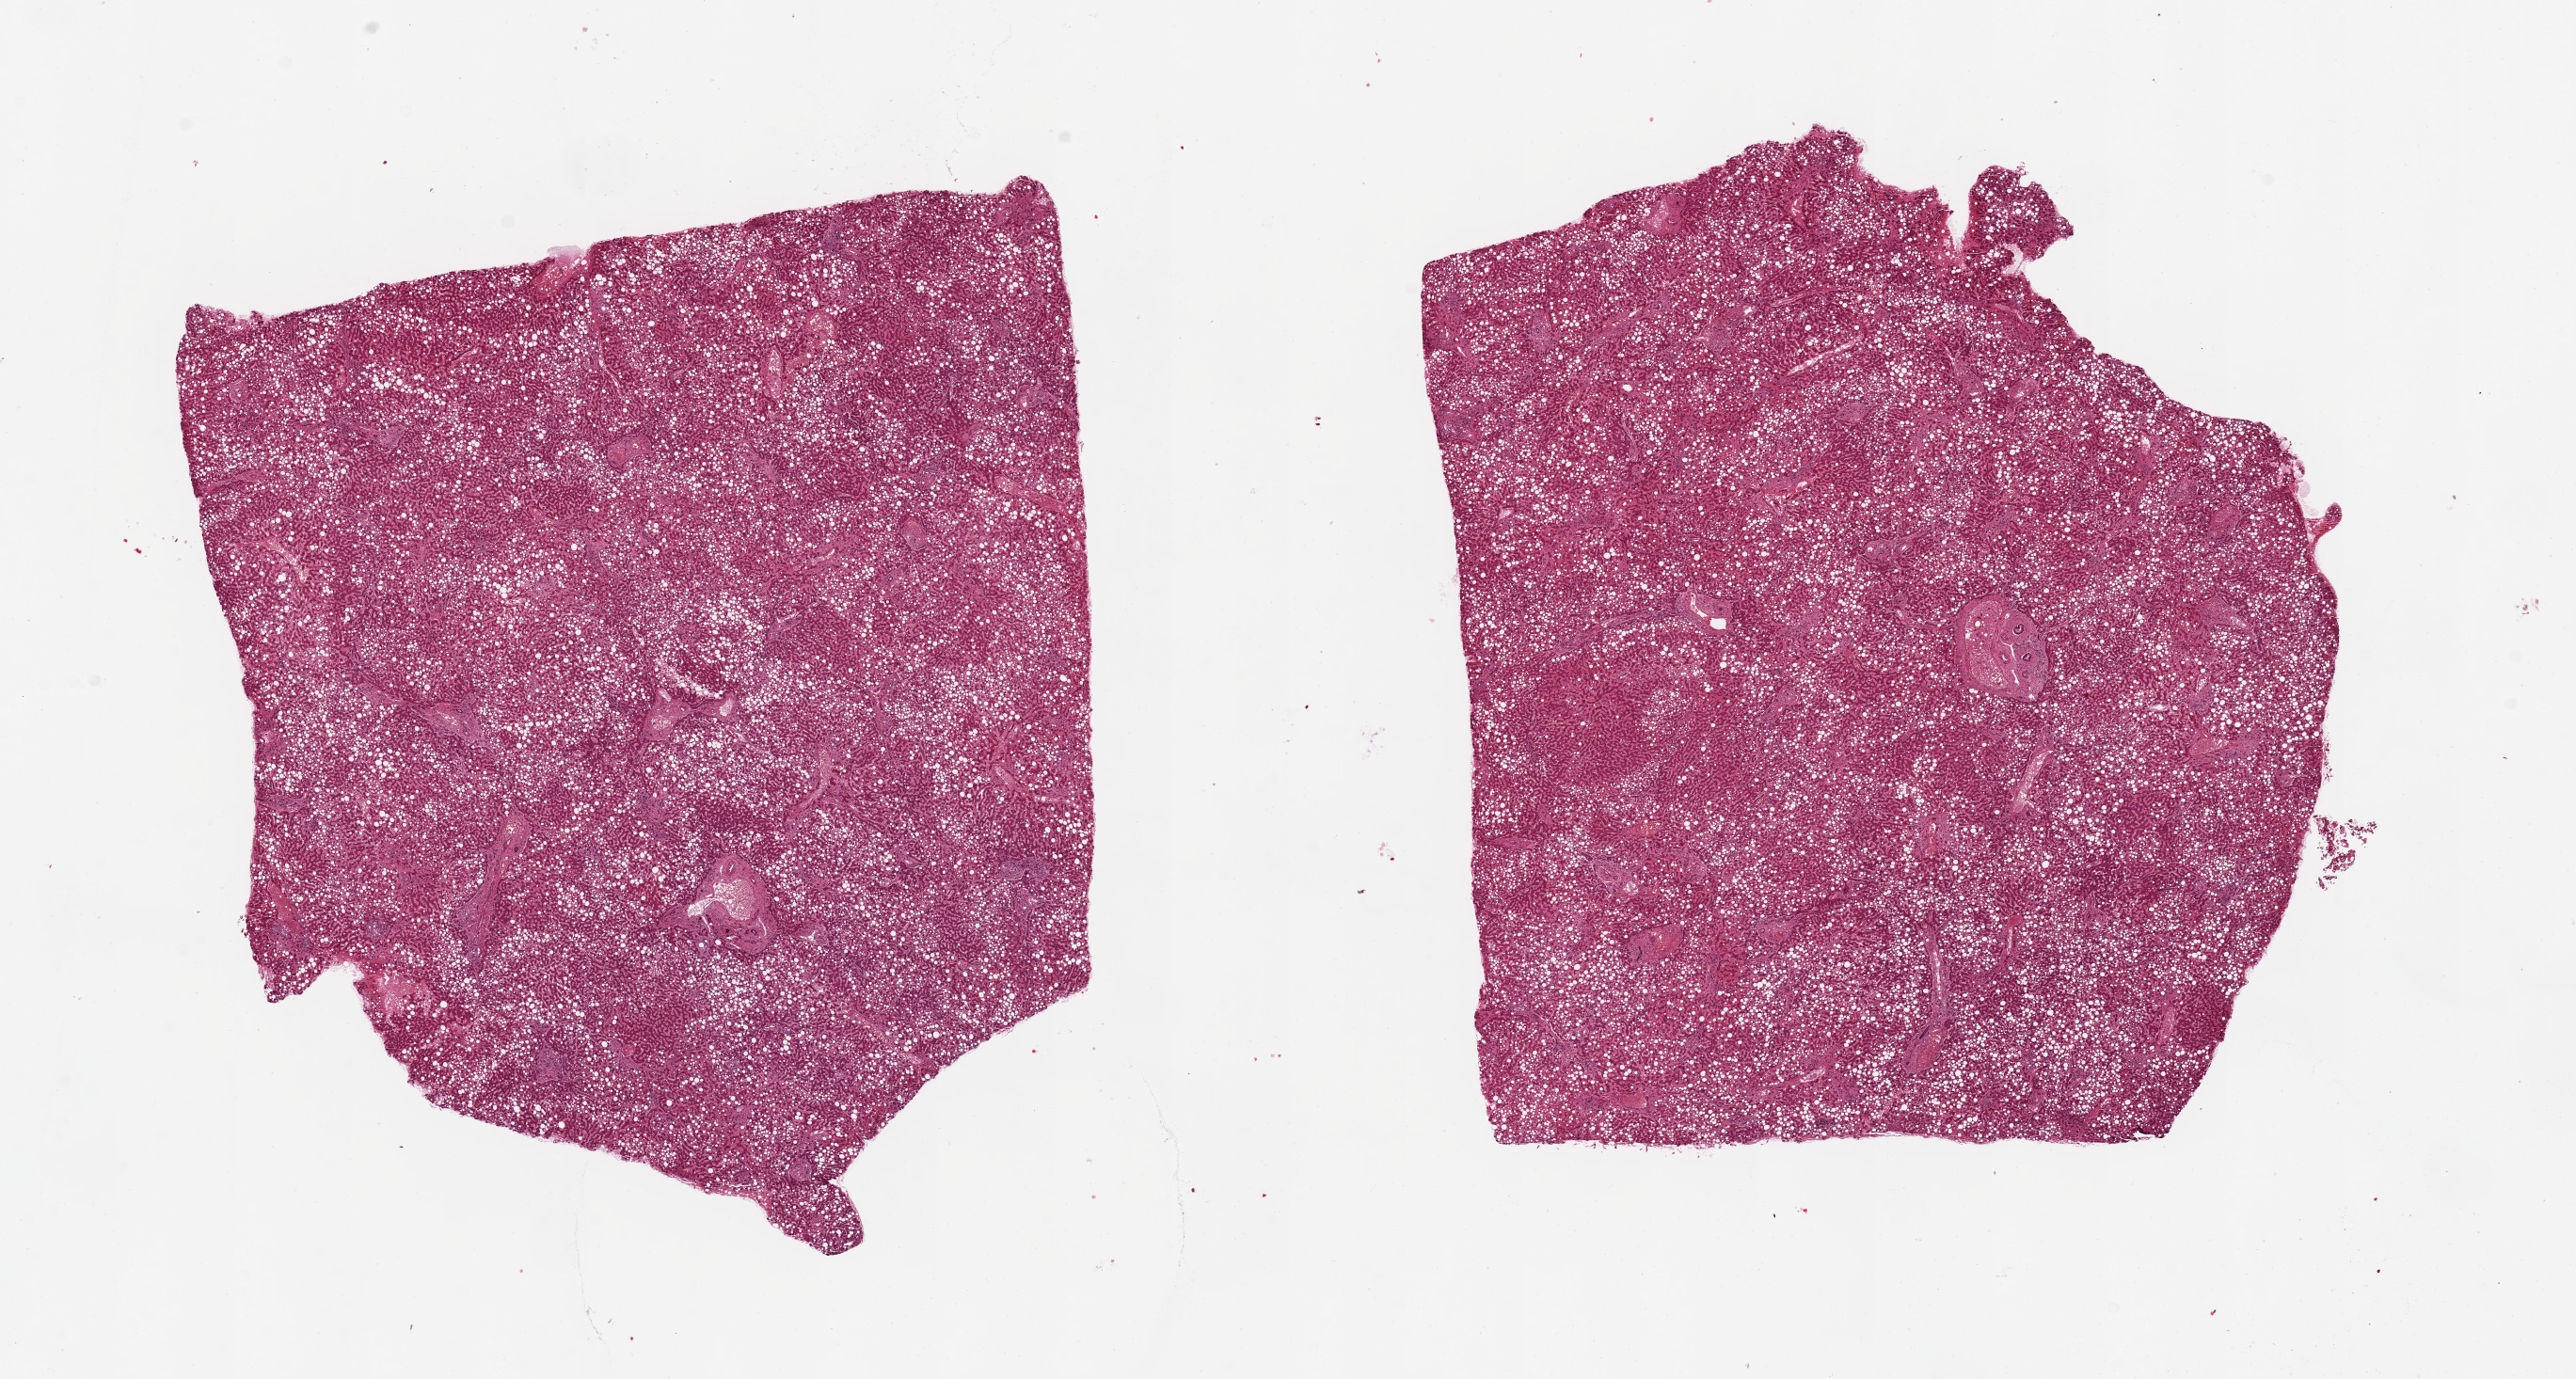
Digitized hematoxylin and eosin (H&E)-stained section, brightfield — low-resolution overview of the scanned area, about 21.7 x 11.6 mm (slide scanned at 20x). PAXgene-fixed, paraffin-embedded tissue. Sampled site (target tissue): liver. Donor tissue sample. Donor sex: male.
* reviewer comment on this tissue sample: 2 pieces, 9x7 & 8x8mm; 70-80% macrovesicular steatosis with patchy bridging fibrosis